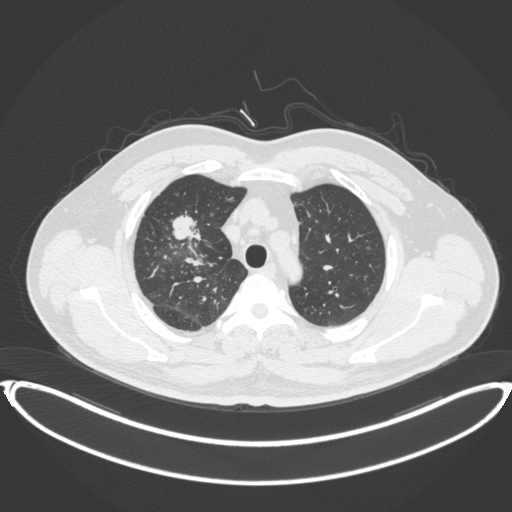
Chest CT, one axial slice; slice 303 of 399 in the series (ordered by position); 120 kVp; lung window (W 1500 / L -600 HU); 1 mm slice thickness; 512 × 512 image matrix. Patient: male, 53 years. From the clinical record (not read from this slice): clinical TNM (as recorded): T2a N0 M0.
Outlined on this slice (bounding box drawn by a radiologist):
- lung tumour (recorded histology: adenocarcinoma): box from (x=170, y=209) to (x=208, y=247) px